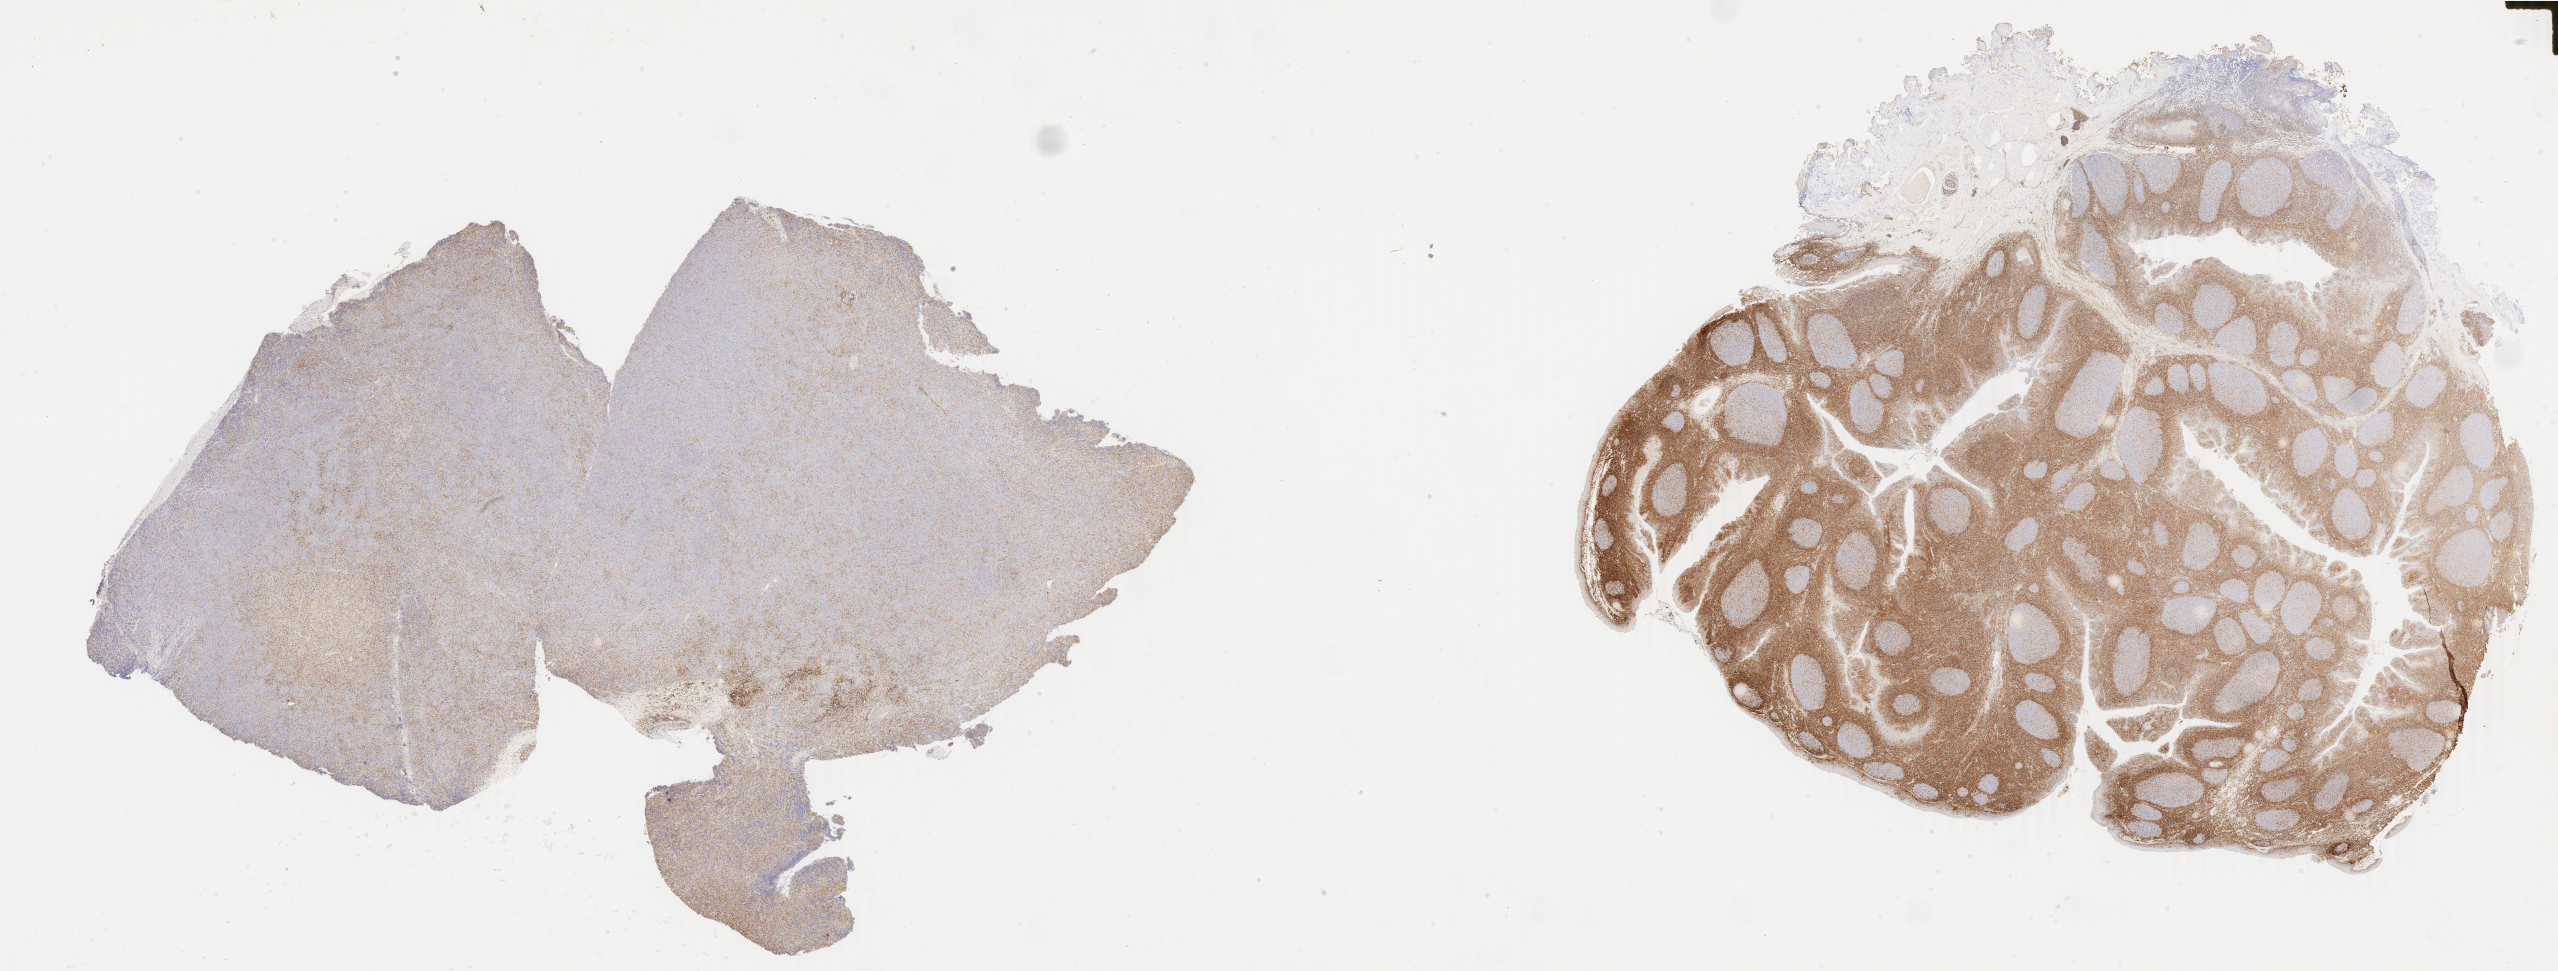
Whole-slide image, immunohistochemical stain for BCL2, shown as a low-resolution overview of the whole scanned area (about 40.7 x 15.4 mm), specimen: tumor tissue. Male, age 7 years at initial diagnosis.
Histologic diagnosis: Diffuse large B-cell lymphoma, NOS.